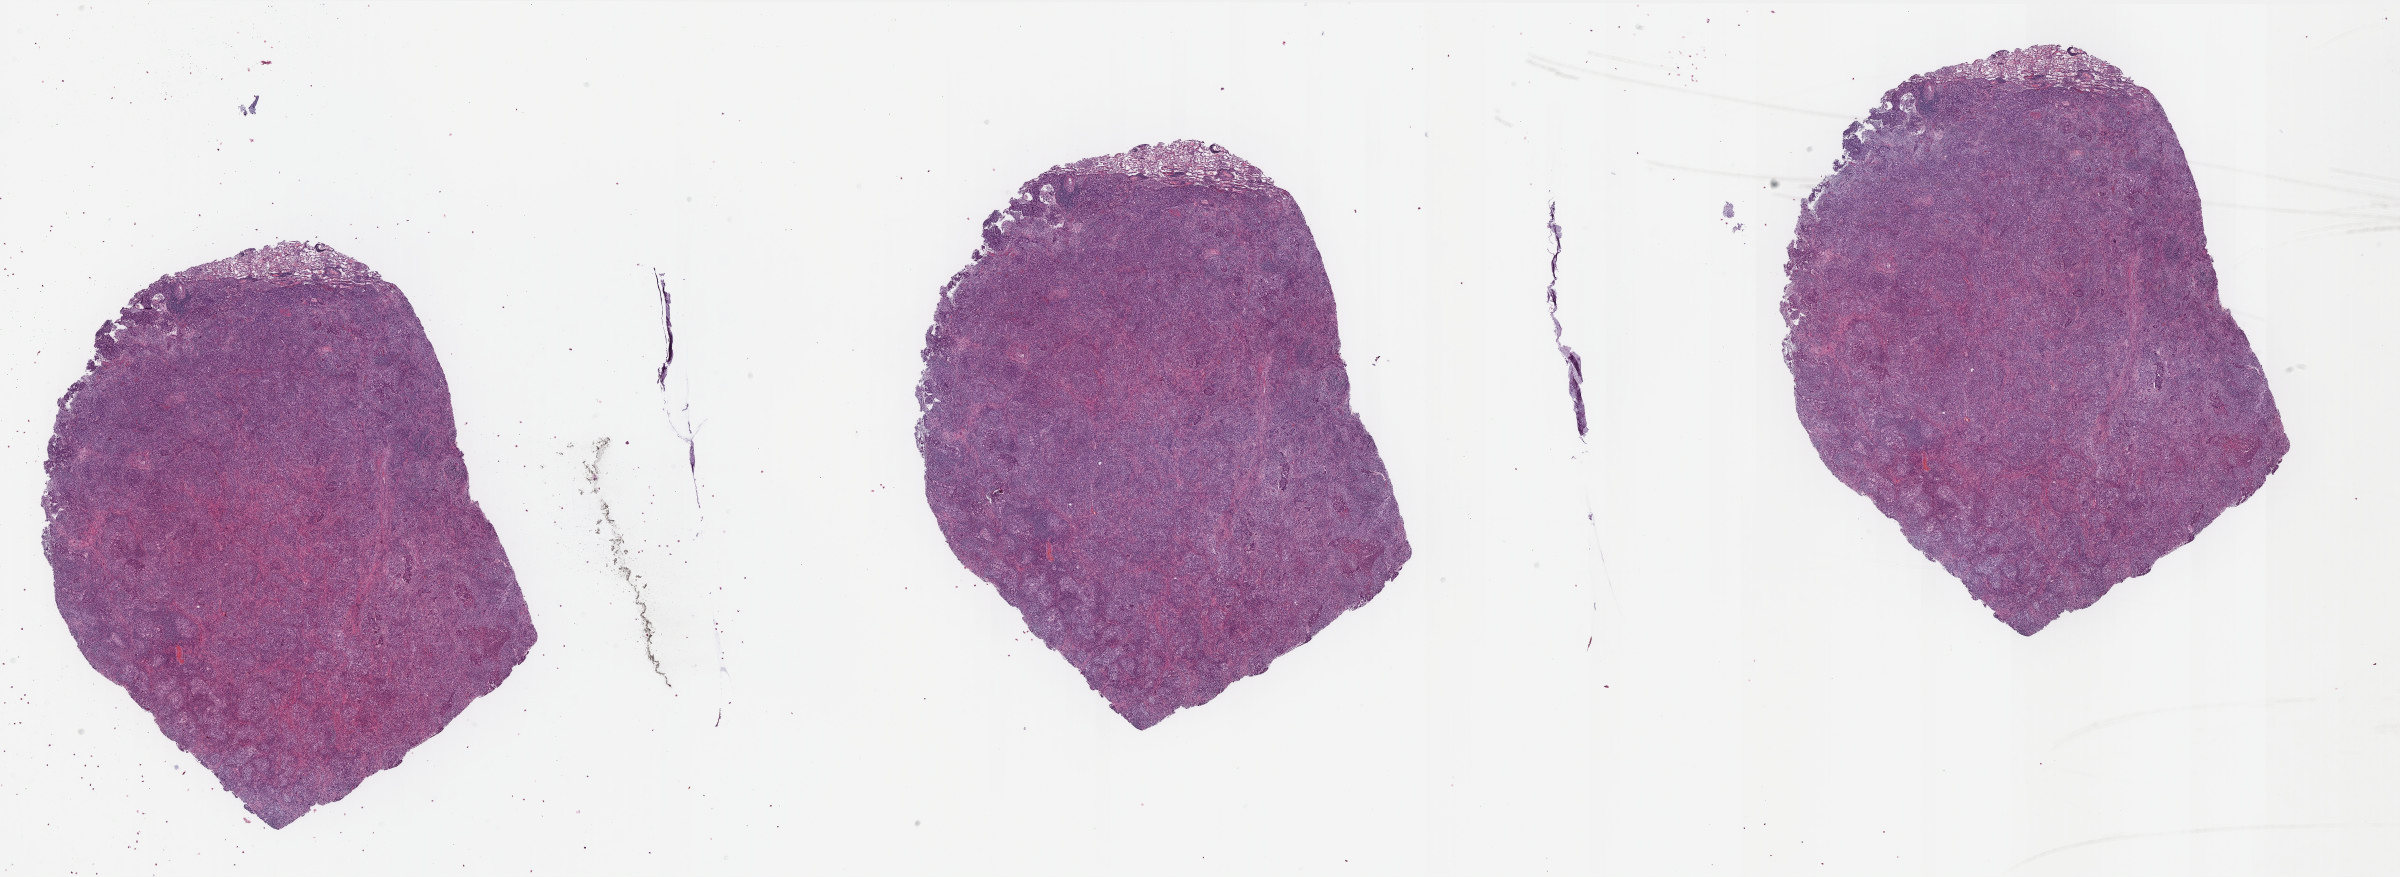
H&E-stained whole-slide image, a low-resolution overview of the entire scanned area, about 38.5 x 14.1 mm (acquisition: 40x scan). Formalin-fixed paraffin-embedded (FFPE) diagnostic section. Primary tumour sample from the lung. Female patient; age at initial diagnosis 73 years.
Laterality: right. AJCC pathologic stage: IB (7th edition). TNM: T2 N0 MX. Histologic diagnosis: Adenocarcinoma, NOS.